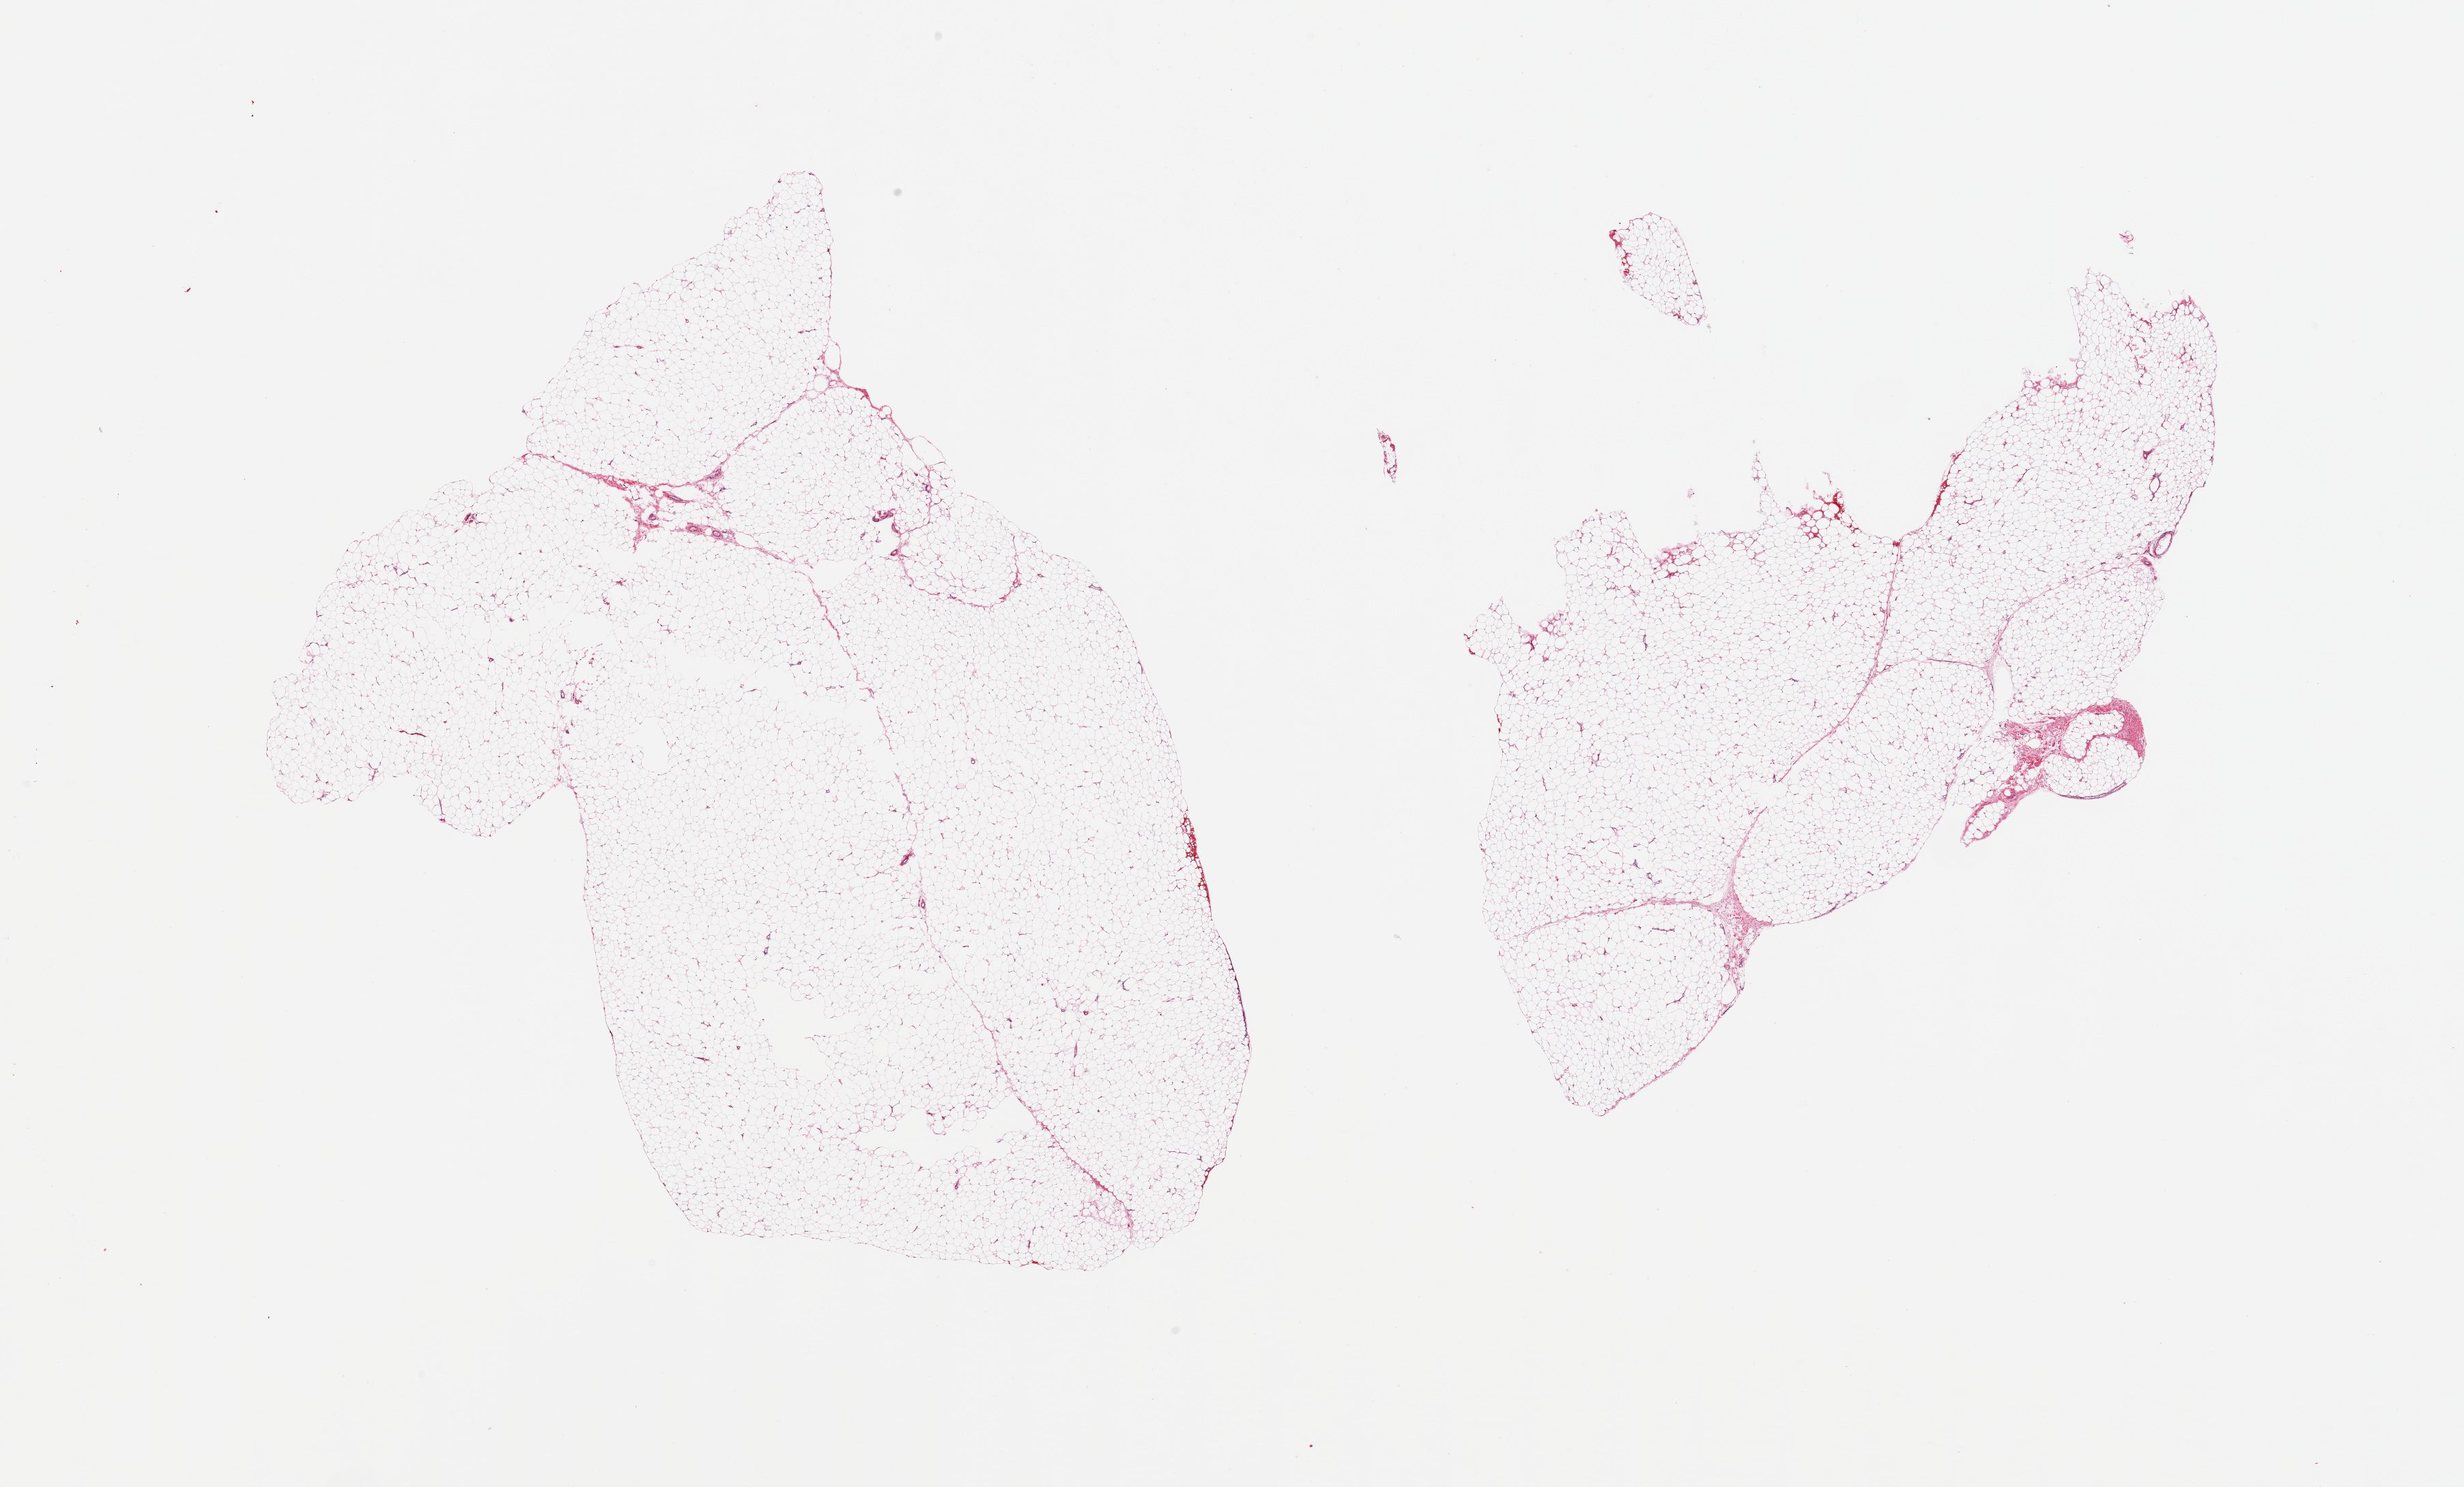
Hematoxylin and eosin (H&E) whole-slide image — a low-resolution overview of the entire scanned area, about 28.5 x 17.2 mm (from a 20x scan); PAXgene-fixed paraffin-embedded (PFPE) section; sampled site (target tissue): adipose tissue; tissue donor sample. Donor: female.
• pathologist's review note for this sample: 2 pieces, trace fascia